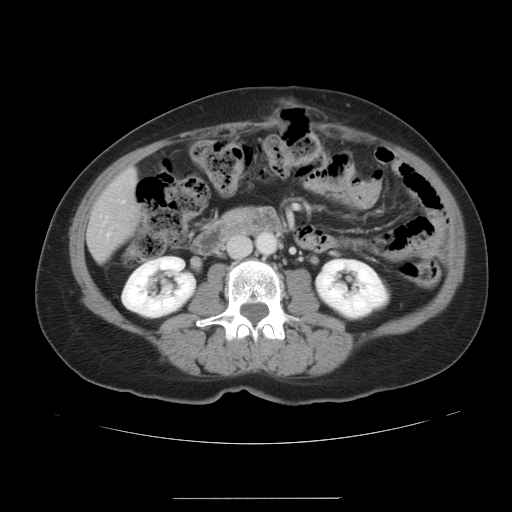
Contrast-enhanced abdominal CT, one axial slice; position 10 of 41 along the scan axis; intravenous contrast given; soft-tissue window (W 400 / L 40 HU); 5 mm slice thickness; 512 × 512 image matrix. Female patient, age 63 years. Case-level facts recorded for this patient, not image findings: diagnosis: colorectal cancer liver metastases, imaged before liver resection; multiple liver metastases: yes; largest metastasis: 1.5 cm; disease in both lobes: yes.
Annotated regions visible in this slice (outlined manually by an expert reader):
- liver: bounding box <89,172,139,259> (left, top, right, bottom; pixels)
- planned liver remnant (the part of the liver to remain after resection): <89,172,139,259>